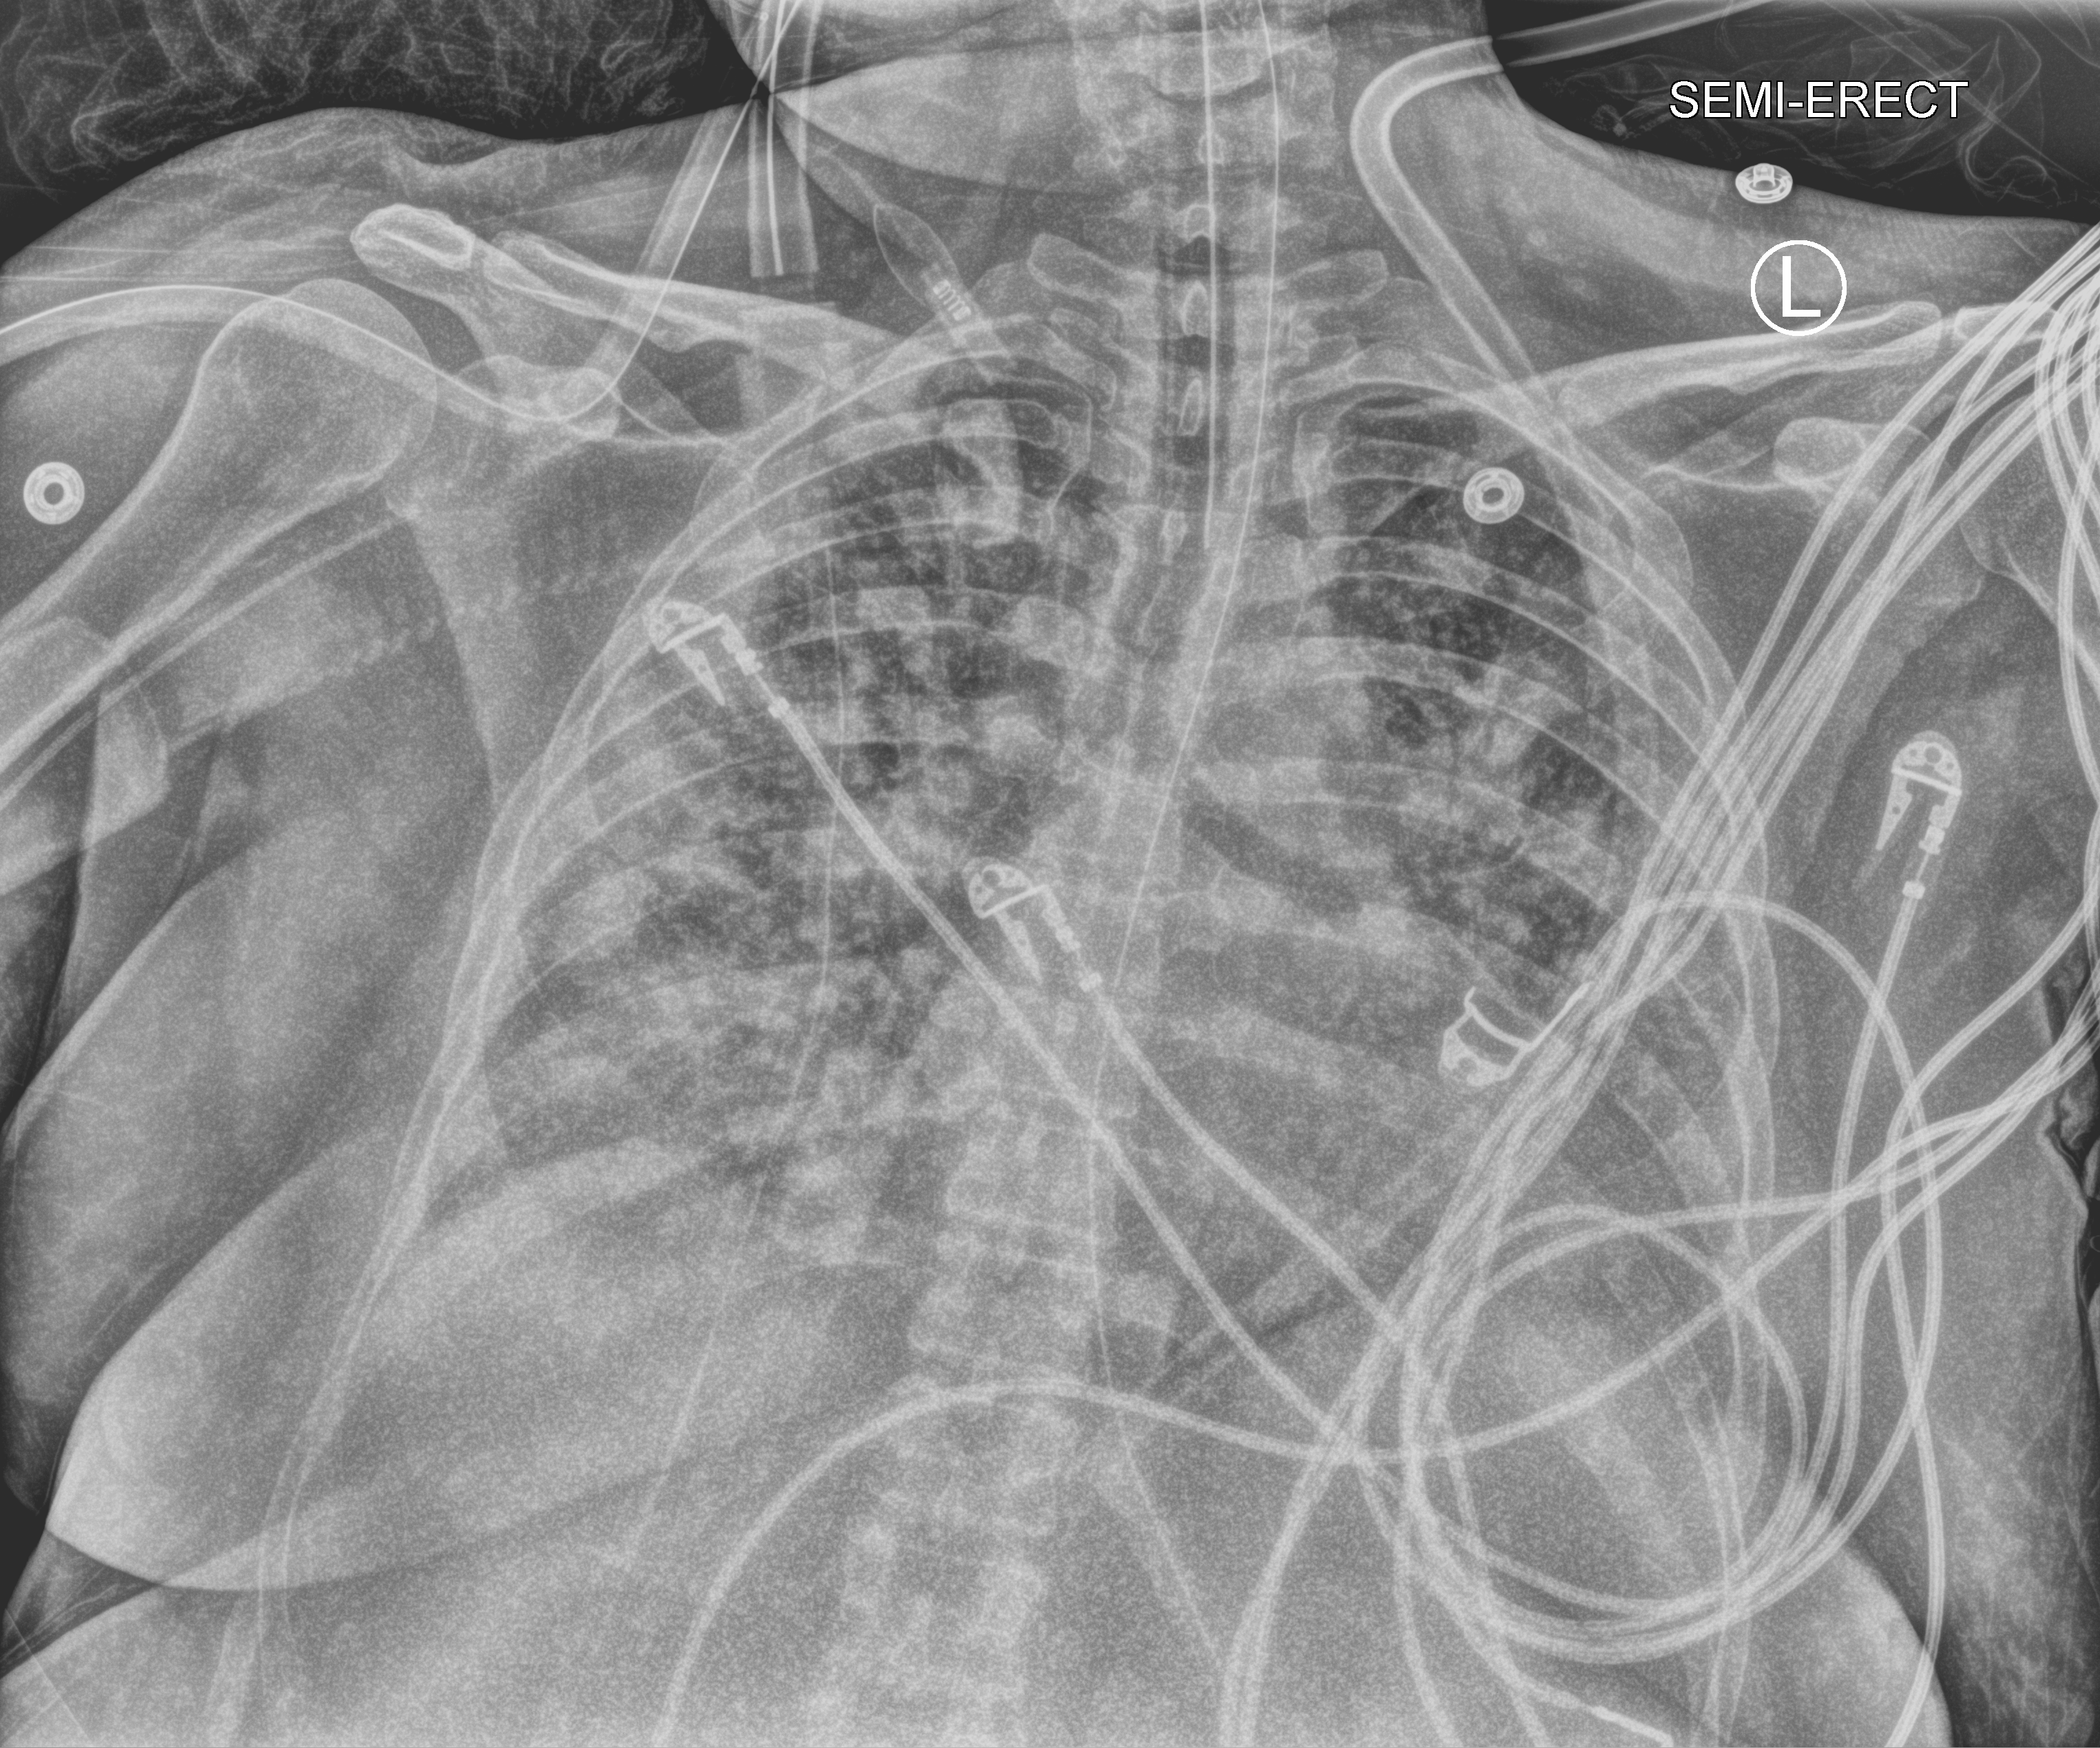
Portable chest radiograph; anteroposterior (AP) projection. Patient hospitalised with COVID-19; female, aged 18–59 years.
Hospital-stay facts (about this admission, not read from this image; timing relative to this image not recorded):
- length of hospital stay: 31 days
- admitted to intensive care during this hospital stay: yes